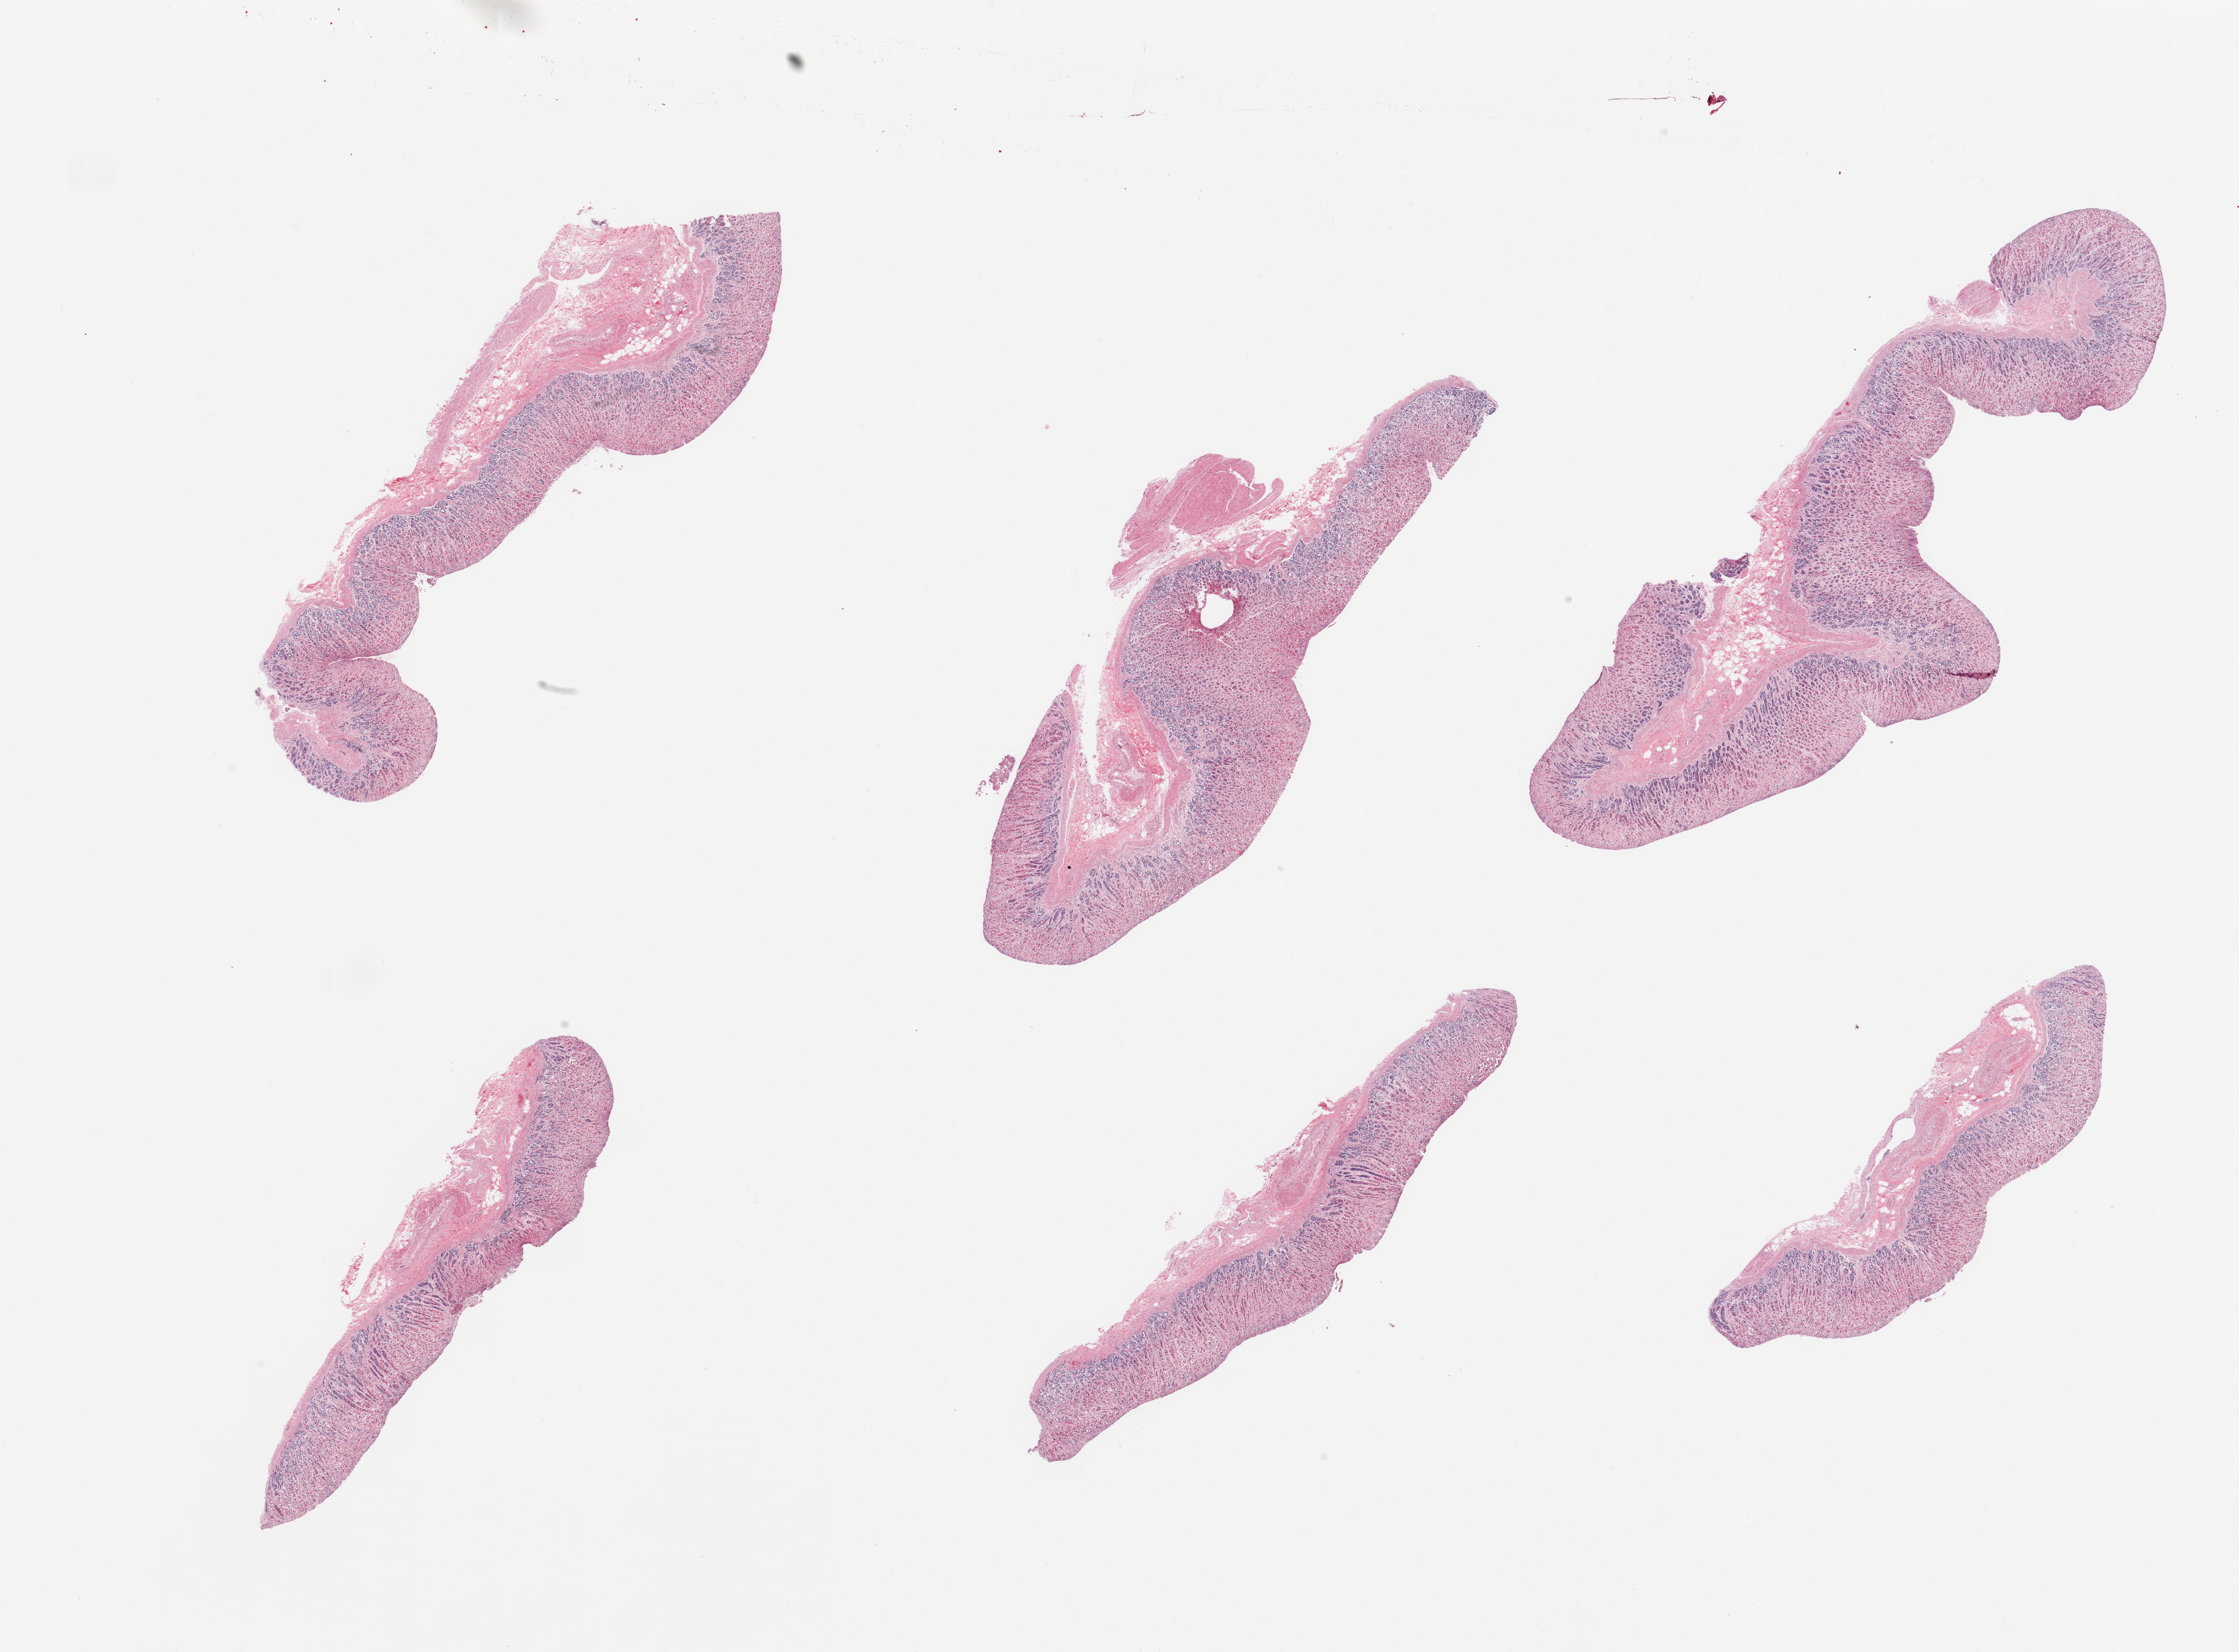
Hematoxylin and eosin (H&E) whole-slide image, brightfield — low-resolution overview of the scanned area, about 26.6 x 19.6 mm; PAXgene-fixed paraffin-embedded (PFPE) section; sampled site (target tissue): stomach; donor tissue sample. Male donor.
Review note (as recorded): 6 pieces; moderately to severely autolyzed gastric mucosa; no muscularis propria.